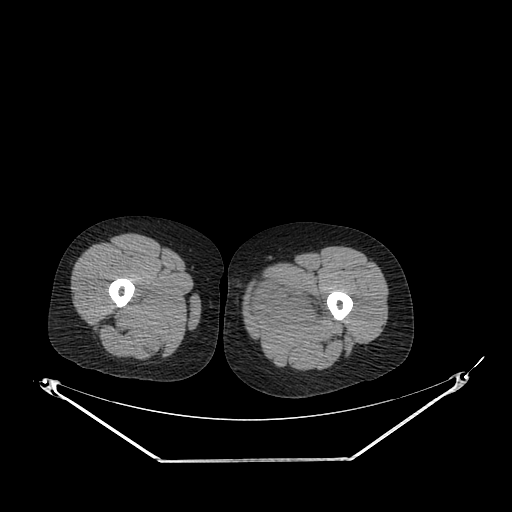
CT of an extremity soft-tissue mass (from a PET/CT study), one axial slice. Position 227 of 267 along the scan axis. Reconstruction kernel SOFT. Soft-tissue window (W 400 / L 40 HU). 3.75 mm slice thickness. 512 × 512 image matrix, field of view 500 × 500 mm. Female patient. From the clinical record (not read from this slice): histological type: pleiomorphic leiomyosarcoma; grade: intermediate; site of the primary tumour: left thigh.
Structures marked on this image (expert contour drawn on MRI and transferred to this co-registered scan by the dataset authors):
- gross tumour volume including surrounding oedema: box from (x=249, y=276) to (x=328, y=323) px
- gross tumour volume (mass): (x=251, y=278)–(x=312, y=323)